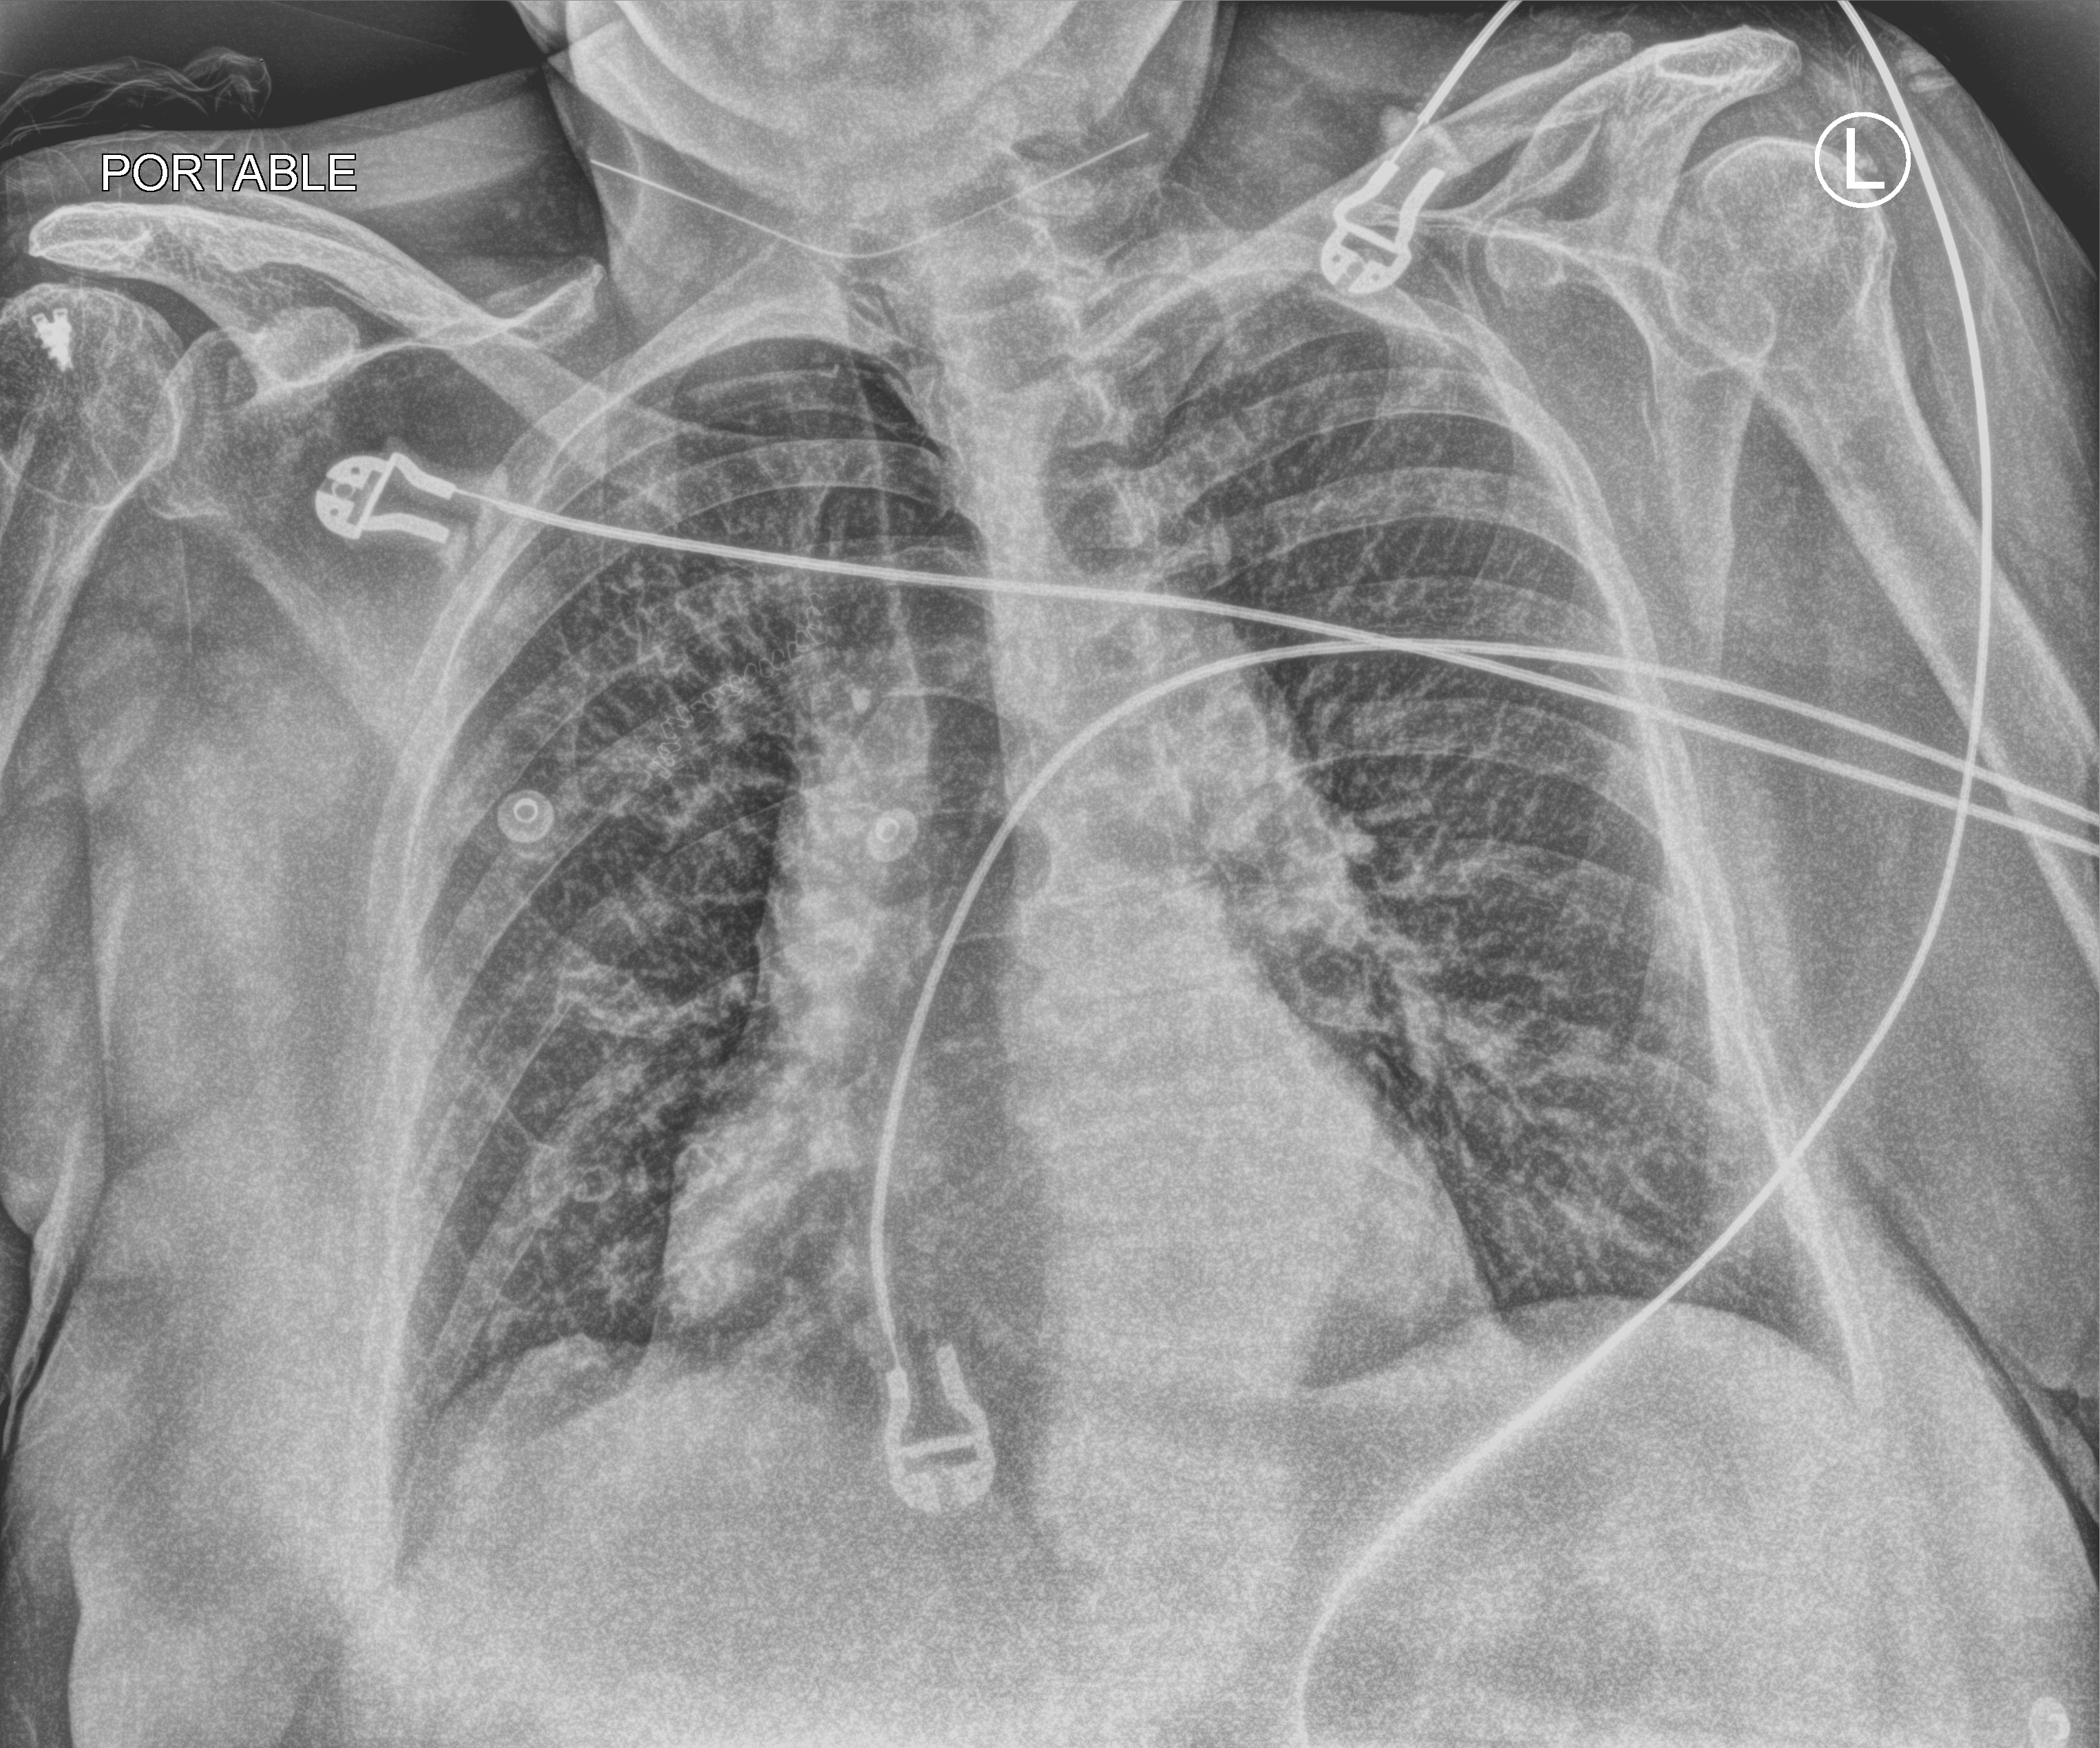
Portable chest radiograph. Patient hospitalised with COVID-19; female, aged 75–90 years.
Hospital-stay facts (about this admission, not read from this image; timing relative to this image not recorded): admitted to intensive care during this hospital stay: no; mechanically ventilated during this hospital stay: no; chronic kidney disease (admission record): no.